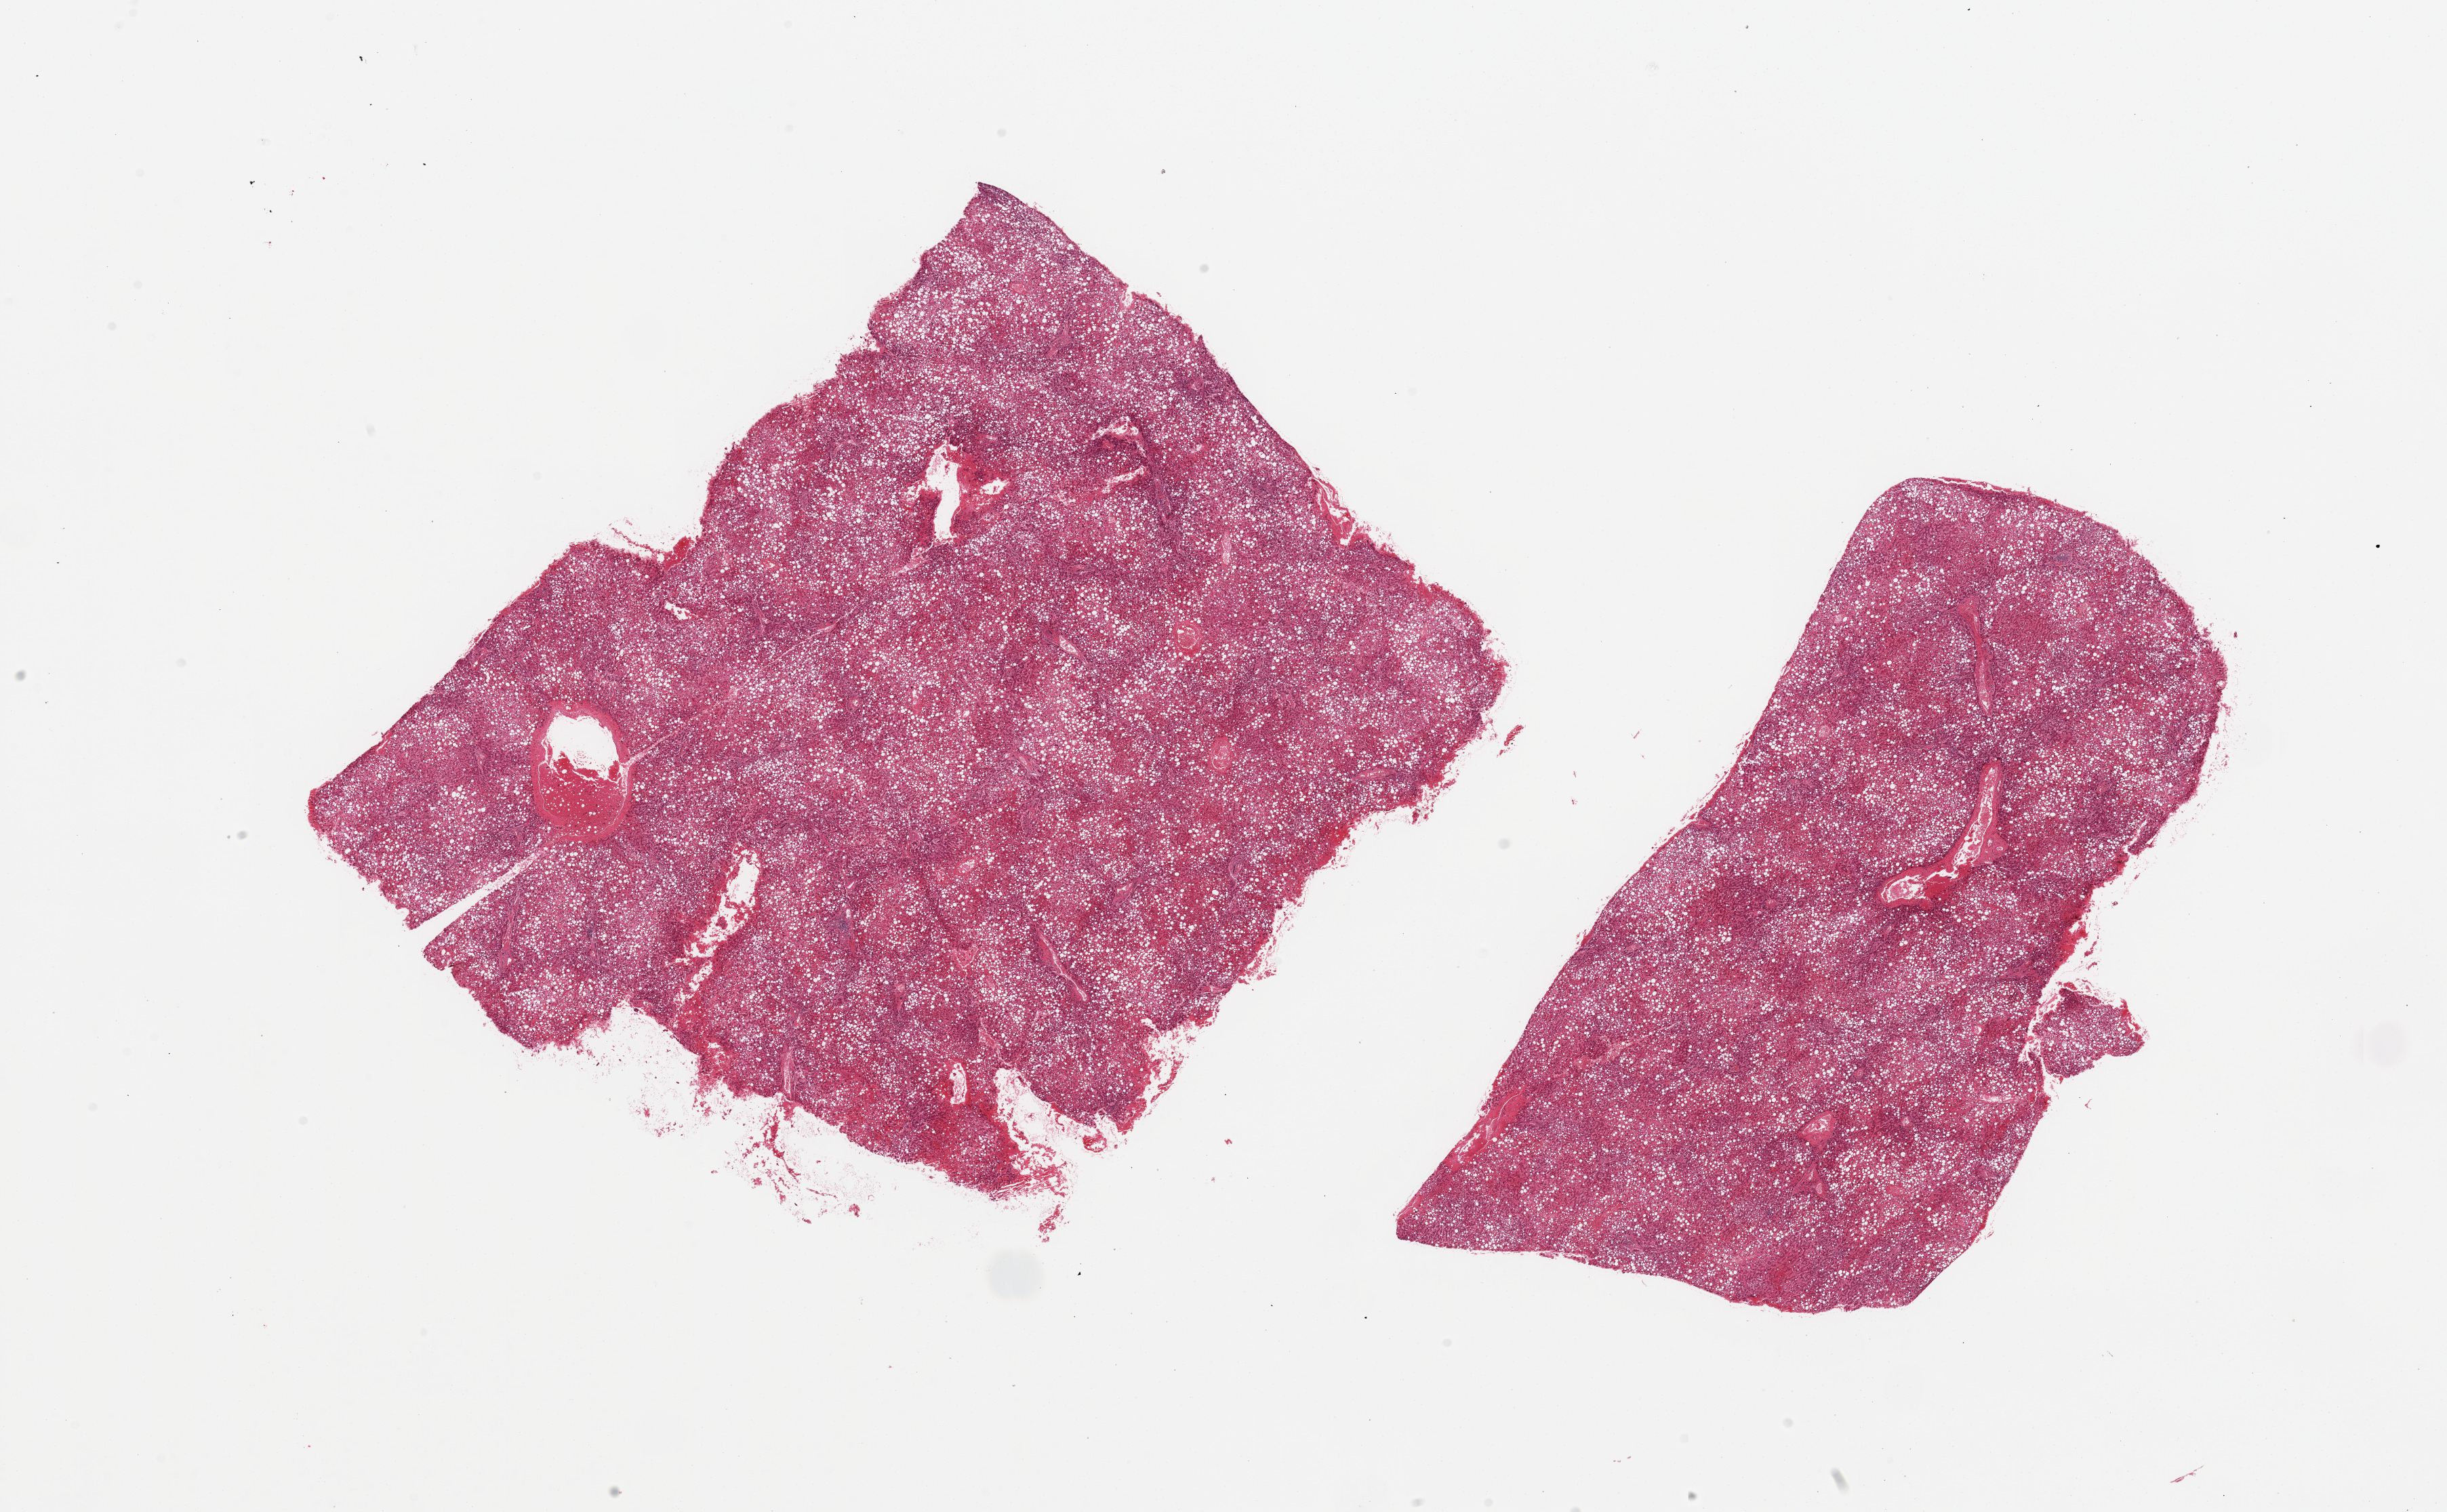
Whole-slide image, H&E stain, a low-resolution overview of the entire scanned area, about 28.5 x 17.6 mm. PAXgene-fixed, paraffin-embedded tissue. Section of liver (target tissue). Tissue donor sample. Donor: male.
Reviewer comment on this tissue sample: 2 pieces, diffuse macrovesicular steatosis involves >80% parenchyma.